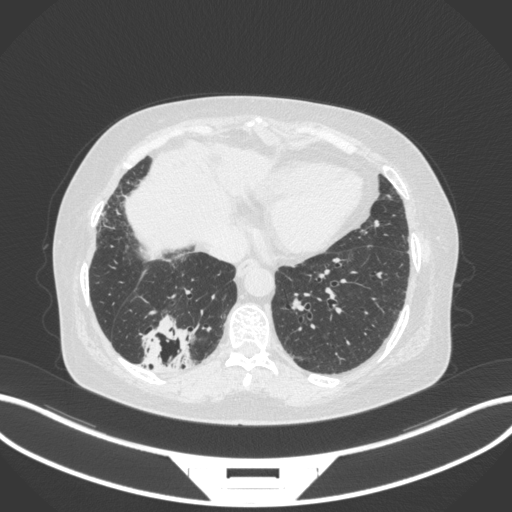
Chest CT, one axial slice. Lung window (W 1500 / L -600 HU). 1 mm slice thickness. 512 × 512 image matrix, field of view 400 × 400 mm. Patient: female, 65 years. Case-level facts recorded for this patient, not image findings: clinical TNM (as recorded): T2b N1 M0.
Outlined on this slice (rectangle marked by the reading radiologist):
- lung tumour (recorded histology: adenocarcinoma): bounding box (x1, y1, x2, y2) in pixels: (137, 311, 194, 375)